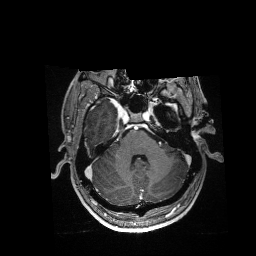
Brain MRI from a brain-tumour surgery series, one axial slice. Slice 119 of 176 in the series (ordered by position). T1-weighted post-contrast. 1 mm slice thickness. 256 × 256 image matrix, field of view 256 × 256 mm. Case-level facts recorded for this patient, not image findings: histopathology: Glioblastoma; WHO grade: 4; IDH mutation: no; tumour location: Left Anterior/Superior Temporal.
Structures marked on this image (manually delineated by an expert):
- residual tumour: bounding box (x1, y1, x2, y2) in pixels: (172, 105, 177, 107)